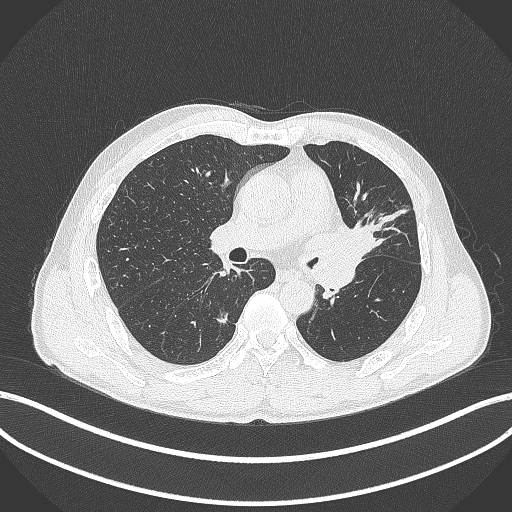
Chest CT, one axial slice. Position 239 of 429 along the scan axis. Reconstruction kernel B70f. Lung window (W 1500 / L -600 HU). 1 mm slice thickness. 512 × 512 image matrix, field of view 400 × 400 mm. Patient: male, 57 years. From the clinical record (not read from this slice): clinical TNM (as recorded): T2b N0 M0.
Outlined on this slice (rectangle marked by the reading radiologist):
- lung tumour (recorded histology: squamous cell carcinoma): bounding box [x1, y1, x2, y2] px = [321, 220, 381, 271]